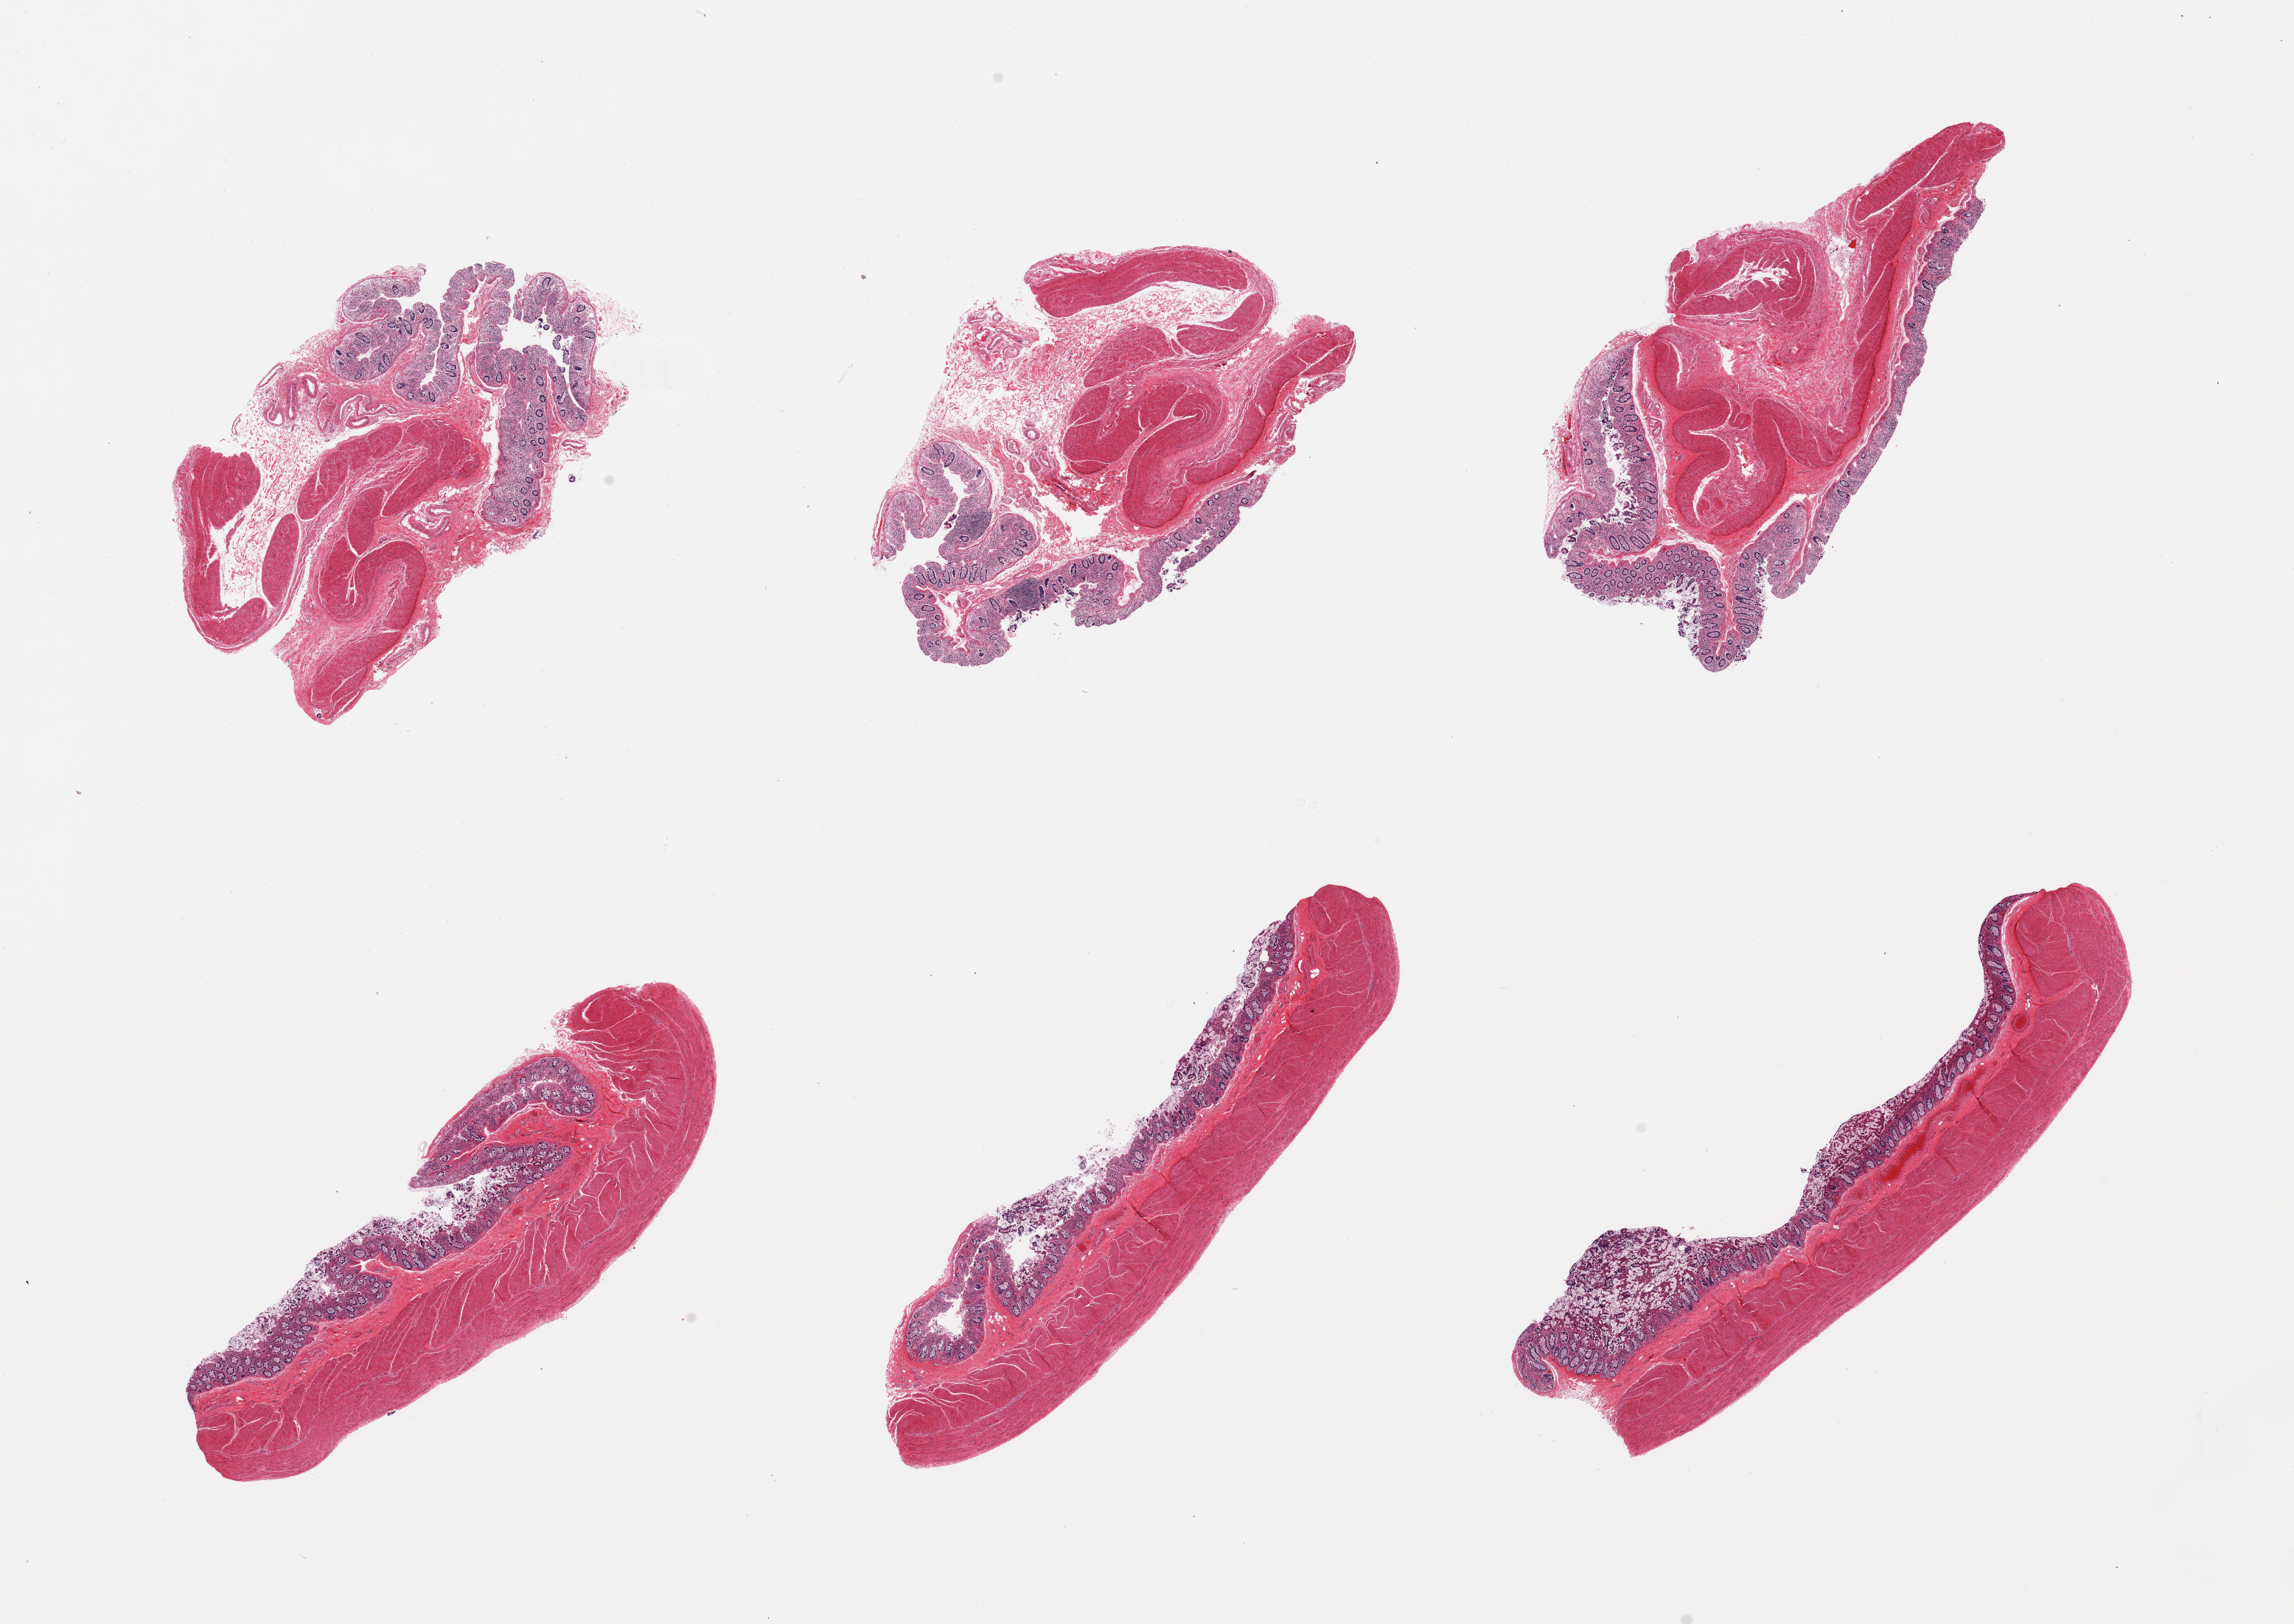
Haematoxylin and eosin whole-slide image — whole scanned area (about 24.6 x 17.4 mm, acquisition: 20x scan) shown as a low-resolution overview. PAXgene-fixed, paraffin-embedded tissue. Sampled site (target tissue): transverse colon. Donor tissue sample. Male donor.
Review note (as recorded): 6 pieces; moderately autolyzed mucosa and muscularis.